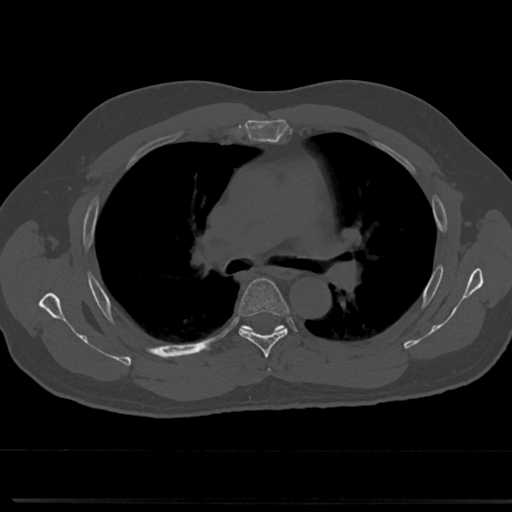
CT including the spine, one axial slice; slice 490 of 817 in the series (ordered by position); reconstruction kernel Br40s/3; 120 kVp; bone window (W 1800 / L 400 HU); 512 × 512 image matrix. Patient: male, 61 years. Case-level facts recorded for this patient, not image findings: primary cancer: prostate.
Outlined on this slice (semi-automatic segmentation, software-assisted and operator-edited):
- T4 vertebra: bounding box (x1, y1, x2, y2) in pixels: (264, 362, 273, 374)
- T5 vertebra: (226, 278, 295, 349)